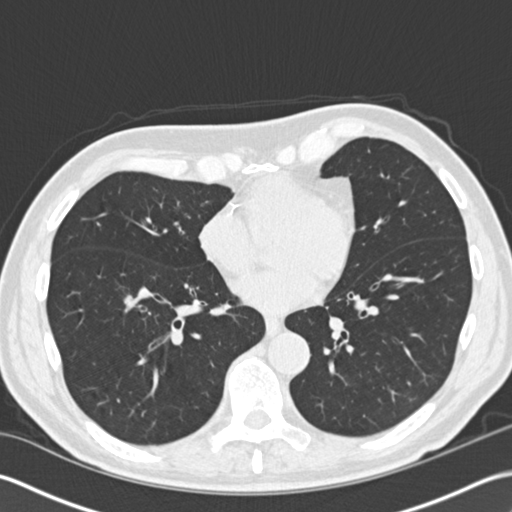
Low-dose screening chest CT, axial slice, first (baseline) screen, lung window (W 1500 / L -600 HU), 2 mm slice thickness, 120 kVp, 512 × 512 image matrix, field of view 350 × 350 mm. Male, age 73 years at enrolment.
Lesion marked by an expert reader, box from (x=95, y=278) to (x=151, y=324) px. Screening reader's record for this exam: no non-calcified nodule ≥4 mm recorded. Official screen result: negative screen, significant abnormalities not suspicious for lung cancer. Later outcome: lung cancer diagnosed 430 days after this screen — non-small cell carcinoma, right lower lobe, stage IA (AJCC 6th edition), 30 mm at pathology.